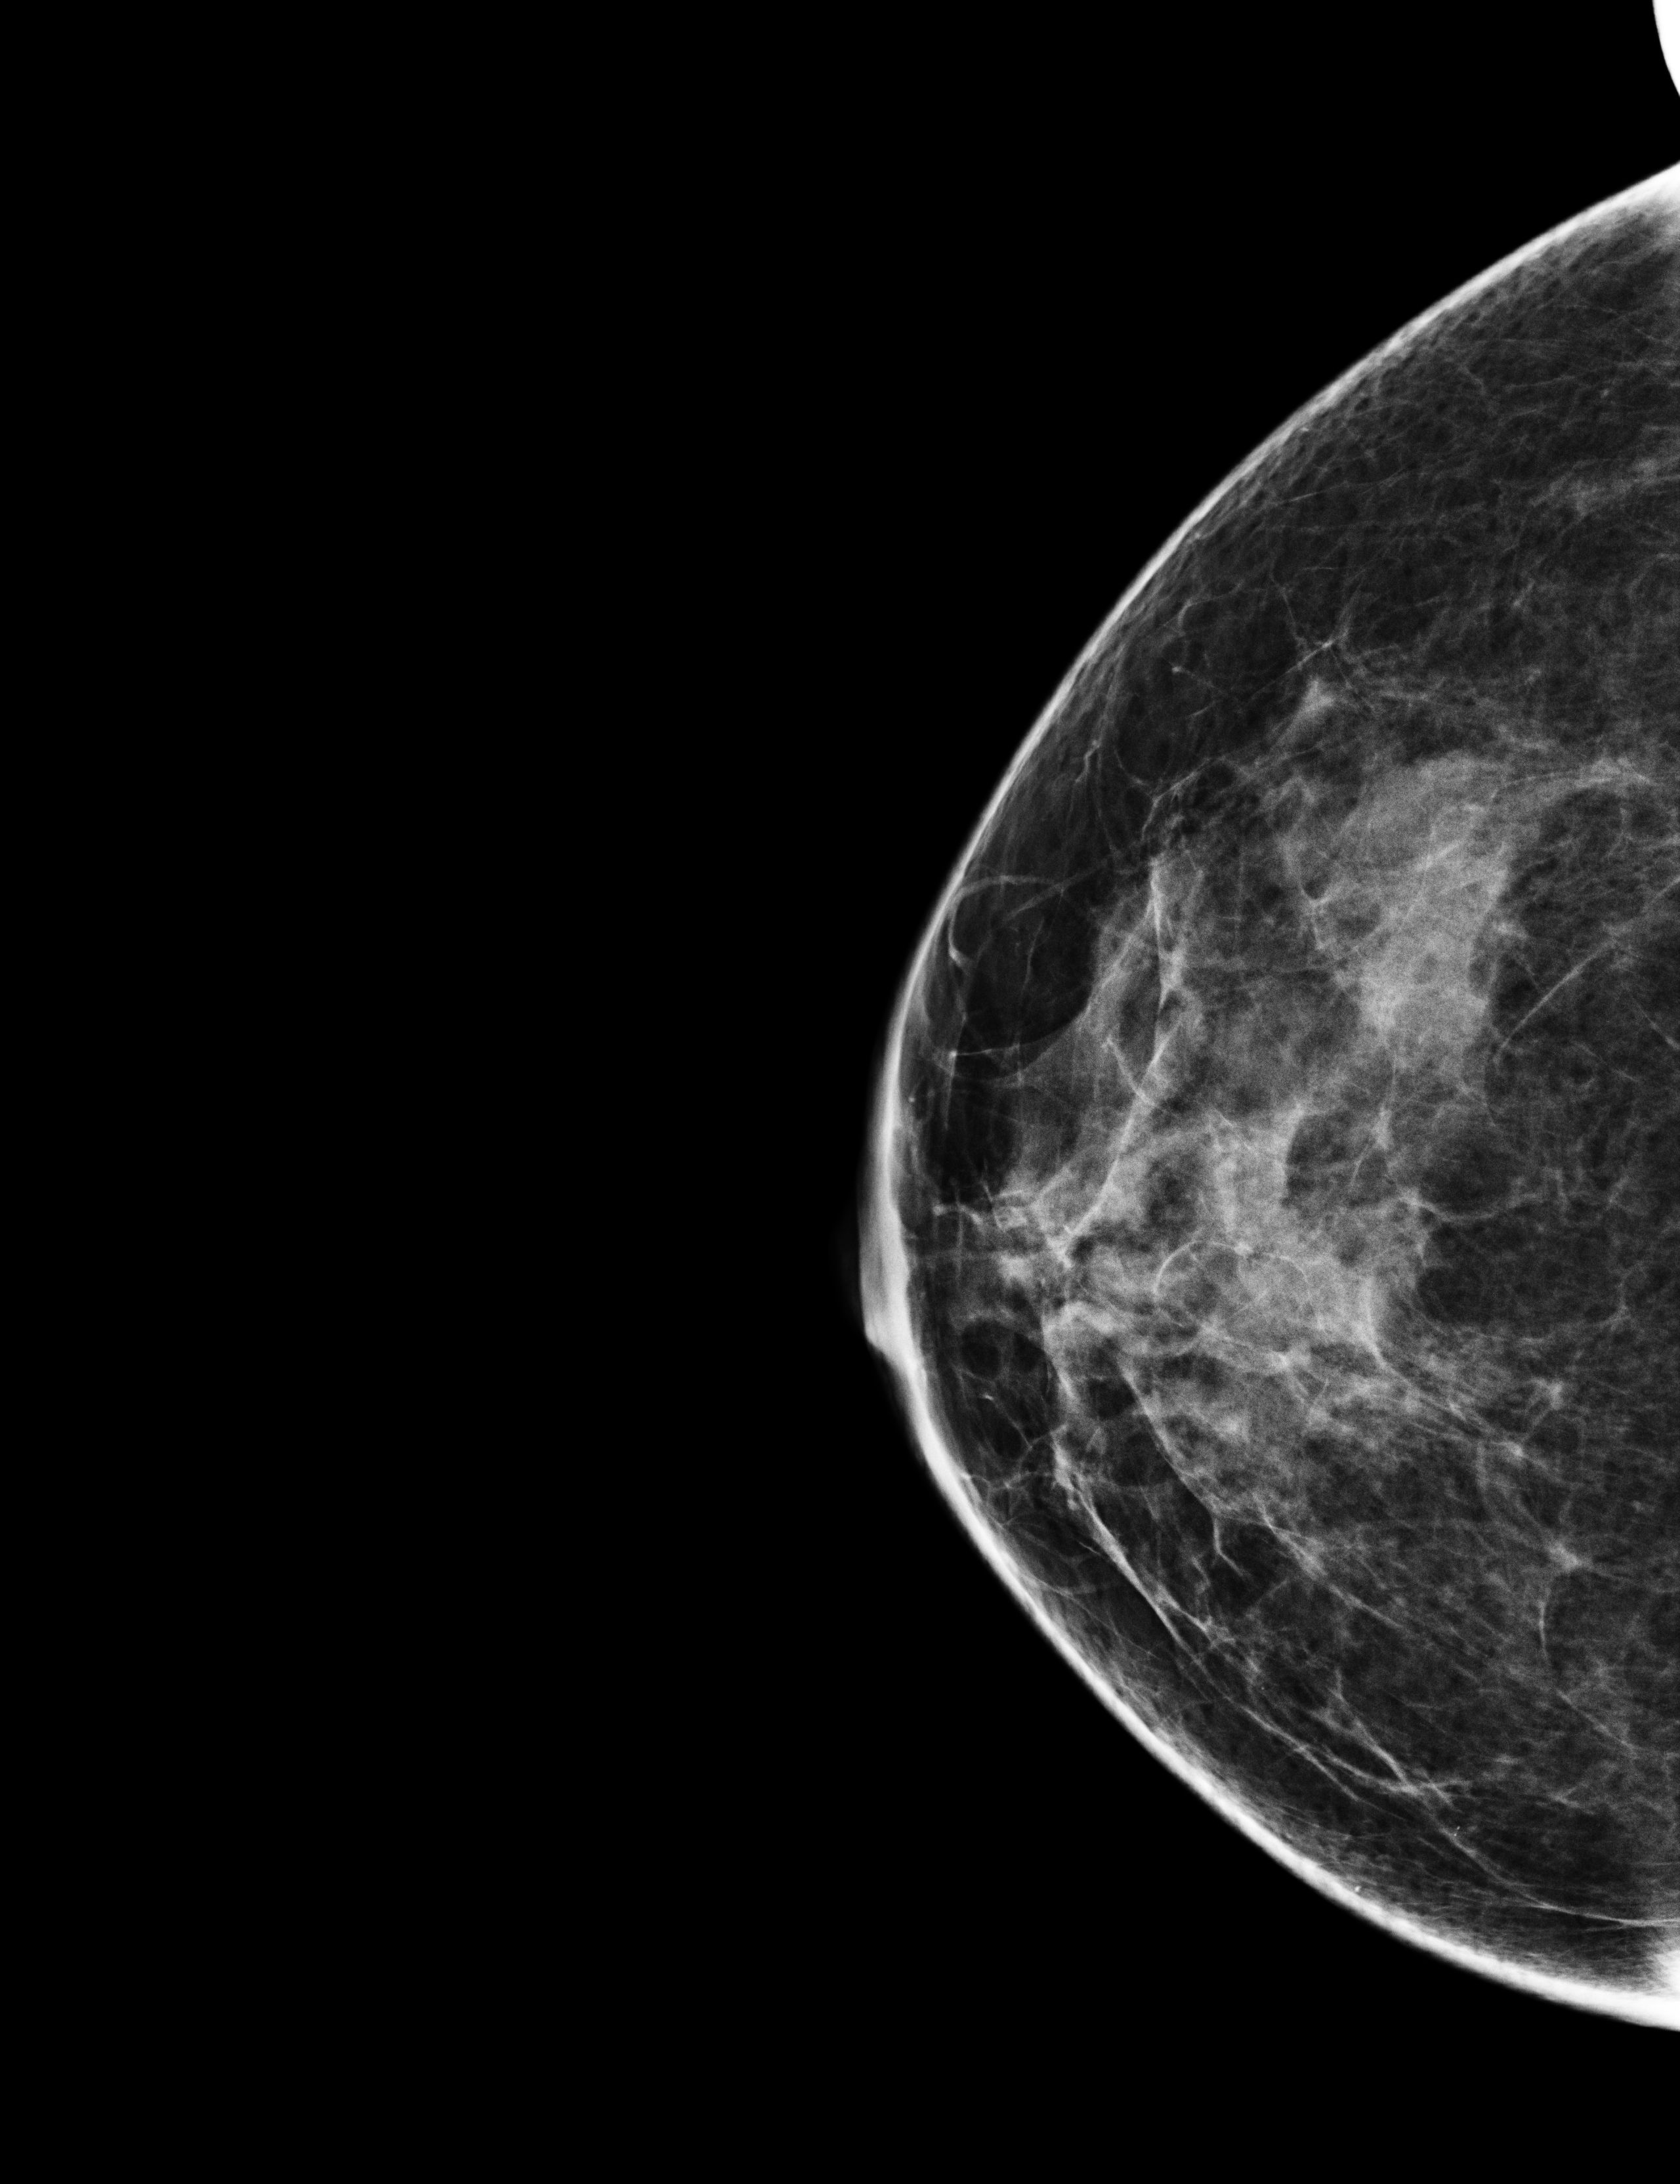
Digital mammogram (FFDM), right breast, CC view, annual screening mammography examination, system: Selenia Dimensions. Patient: female, 46 years.
- BI-RADS breast density category at the screening exam (both breasts, scale 1–4): 3
- final BI-RADS category for the screening round (tomosynthesis exam, both breasts): category 2
- recall: no recall after this screen